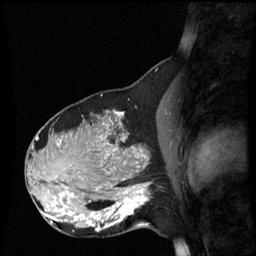
Breast MRI (dynamic contrast-enhanced), one sagittal slice; dynamic contrast-enhanced series, image 2 of 3 at this slice position (ordered by acquisition); 1.5 T; TE 4.2 ms, TR 8.9 ms; 2.2 mm slice thickness; 256 × 256 image matrix, field of view 220 × 220 mm. Female patient, age 31 years. Case-level facts recorded for this patient, not image findings: setting: breast cancer imaged before/during neoadjuvant chemotherapy; receptor status: HR-positive, HER2-negative.
Structures marked on this image (semi-automatic segmentation, software-assisted and operator-edited):
- analysis volume of interest (the breast-tissue region the enhancement analysis was run in; not a lesion): bounding box (x1, y1, x2, y2) in pixels: (90, 180, 152, 235)
- tumour enhancement mask (voxels above the 70 % enhancement threshold inside the analysis volume of interest): (90, 184, 149, 231)